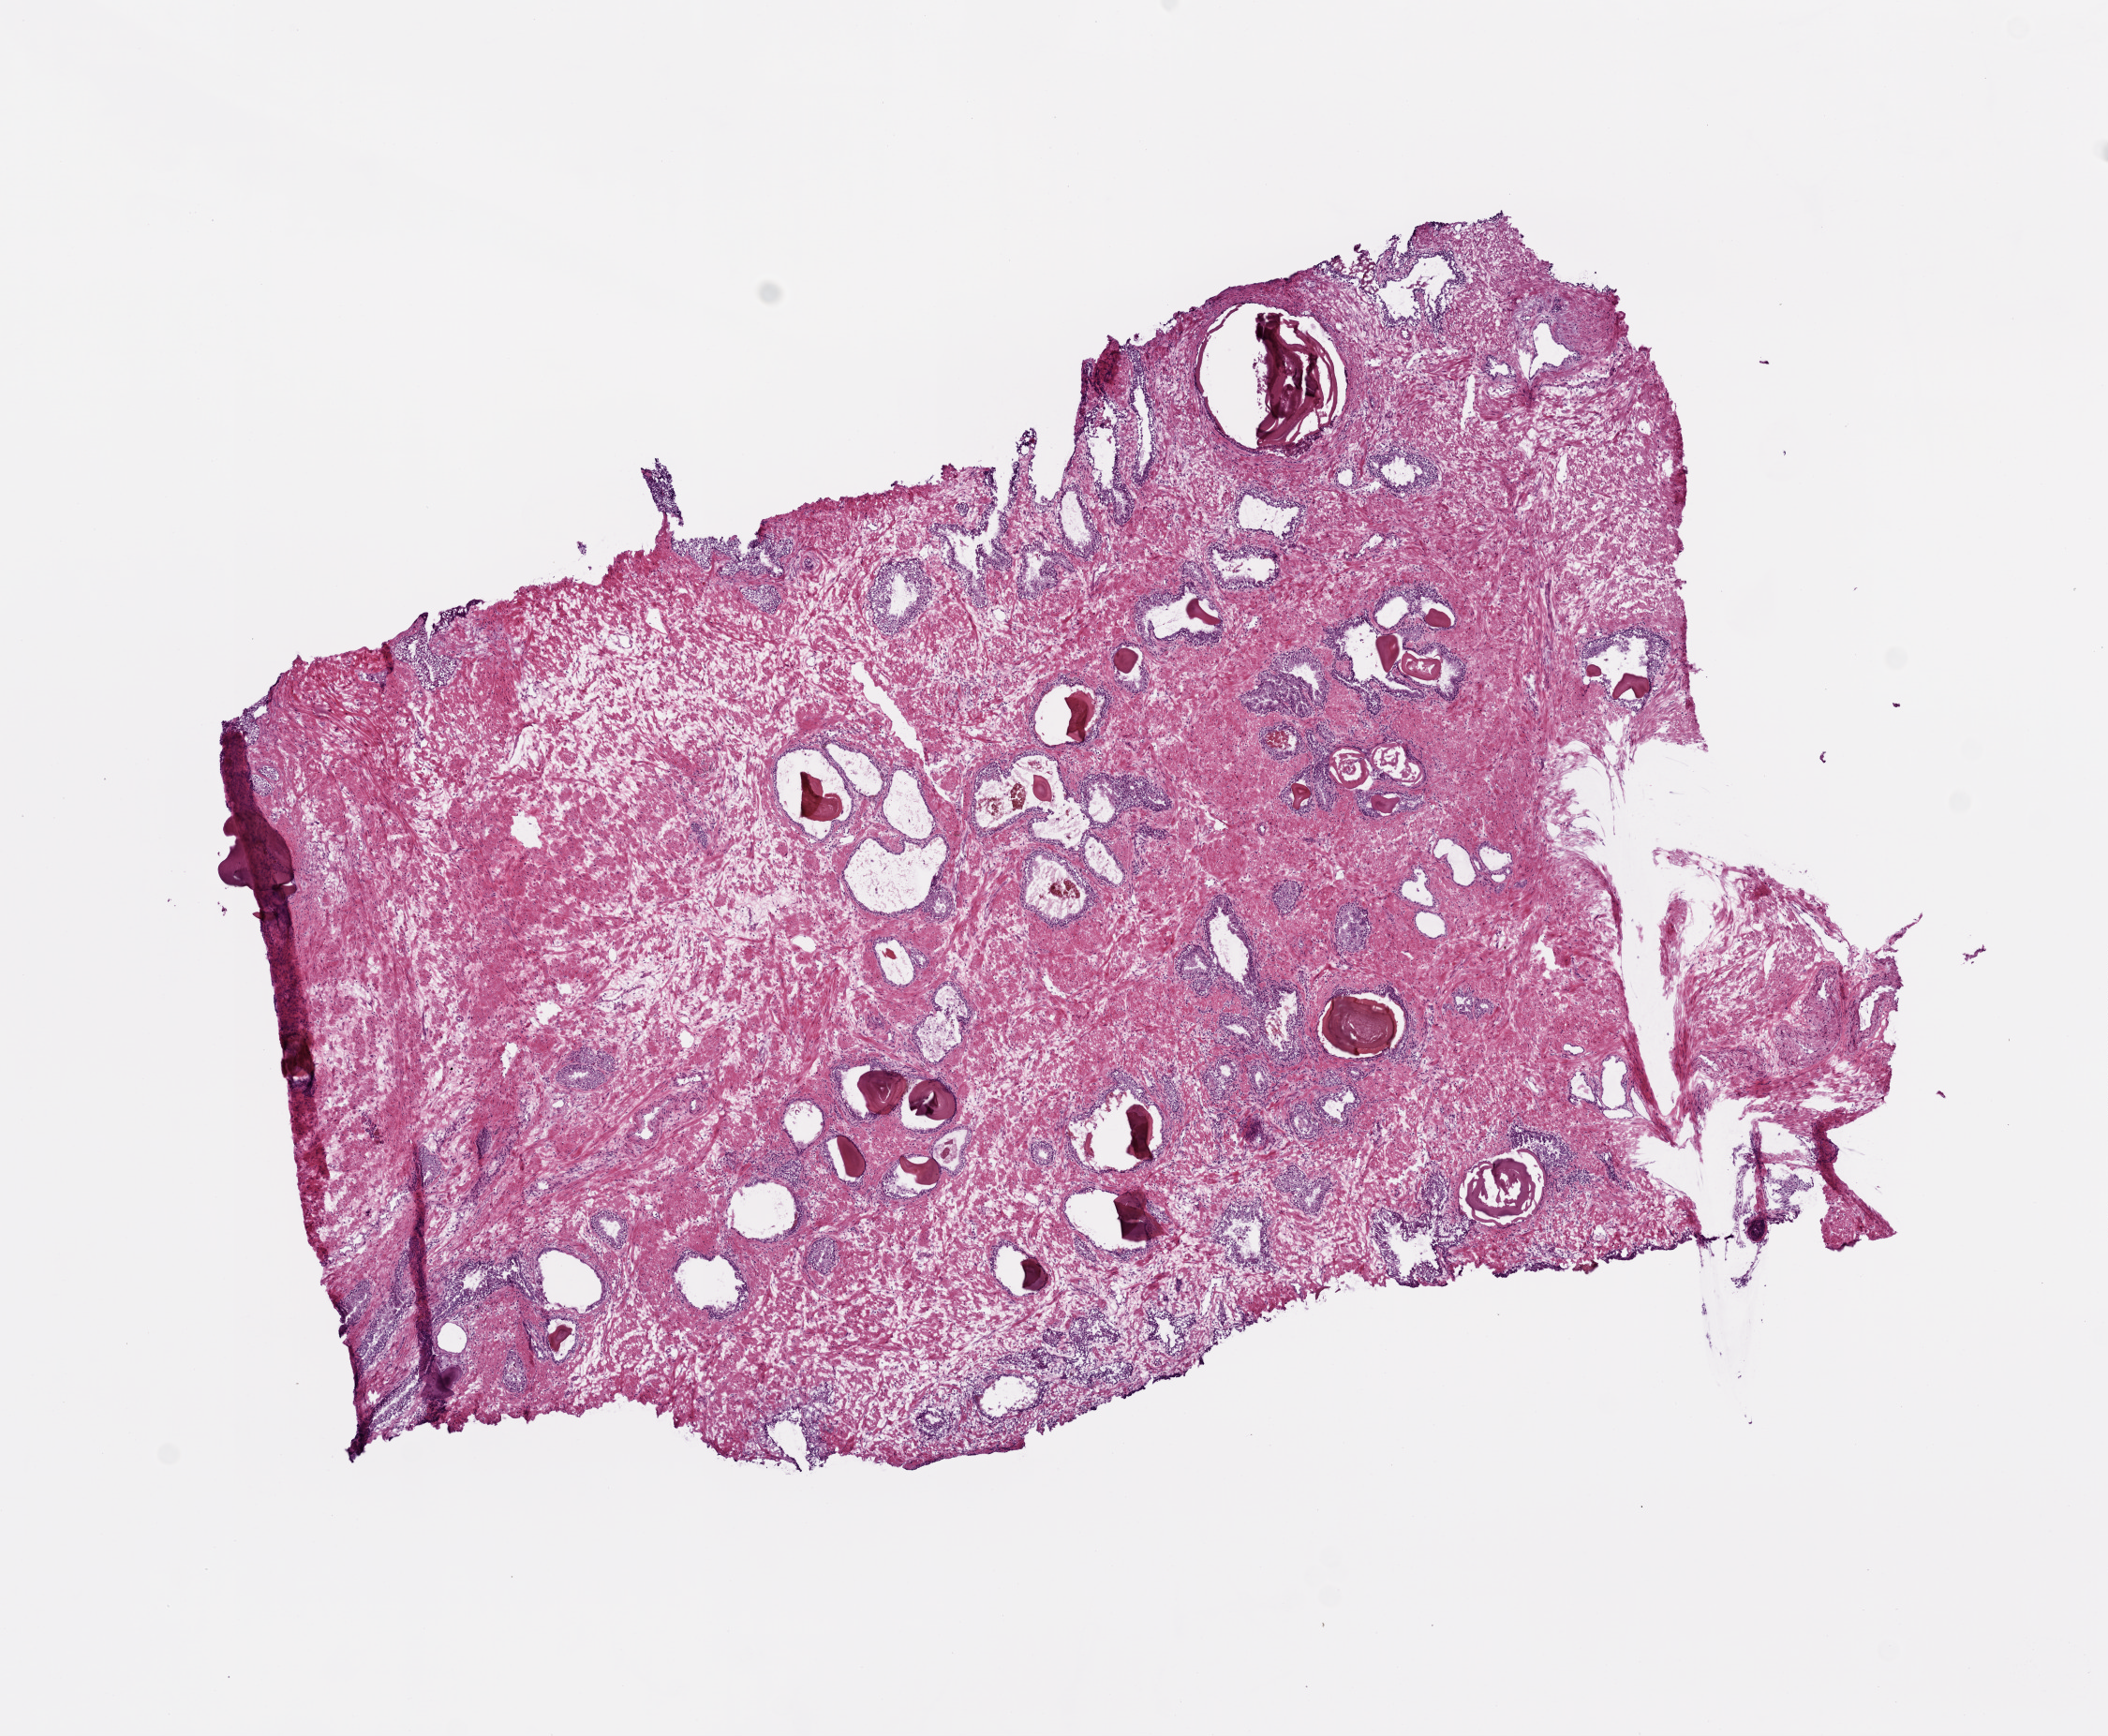
Digitized Hematoxylin and eosin (H&E) stained tissue section (whole slide), a low-resolution overview of the entire scanned area, about 9.0 x 7.4 mm (from a 20x scan); frozen section from the top of the tissue portion; sample: solid tissue normal (non-tumour tissue), prostate. Male, age 60 years at initial diagnosis.
This section: solid tissue normal sample (biorepository sample class). Patient diagnosis: Acinar cell carcinoma (prostate gland).